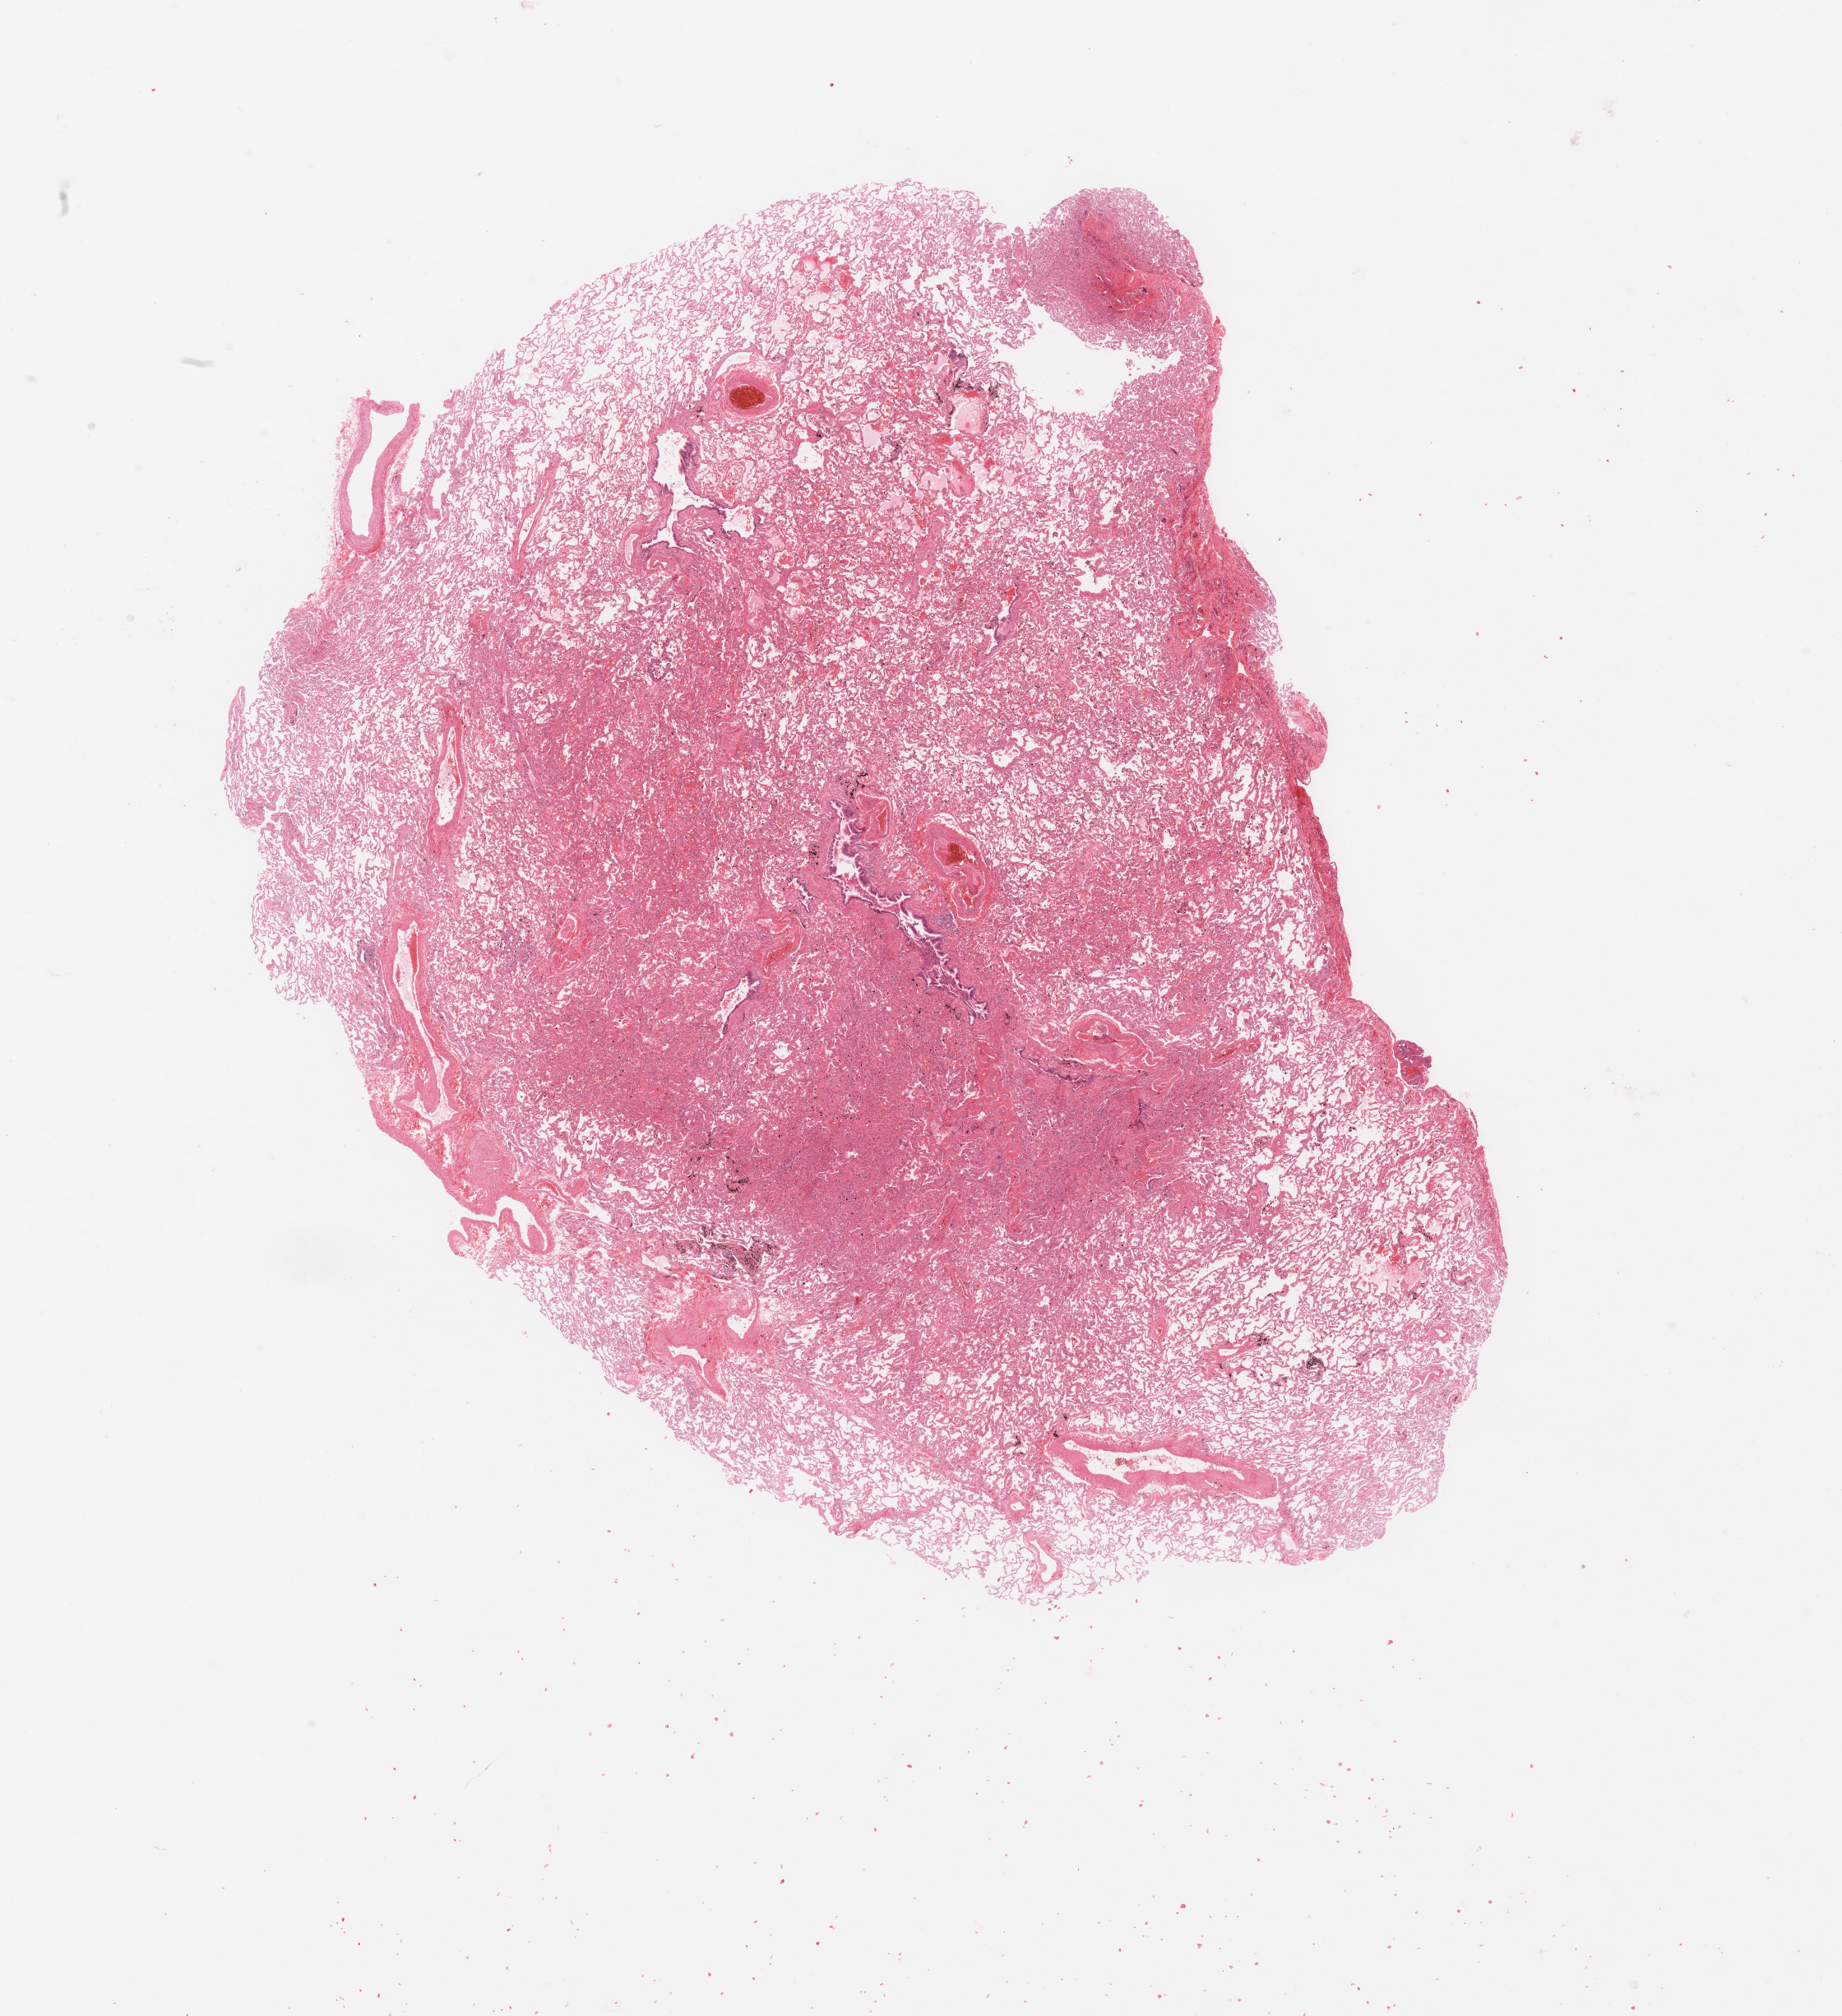
Whole-slide histology image, H&E — whole scanned area (about 17.7 x 19.4 mm, from a 20x scan) shown as a low-resolution overview. Normal (non-tumour) tissue sample, sampled site: lung. 62-year-old female patient.
This section: normal (non-tumour) tissue from the same patient. Patient diagnosis: Adenocarcinoma, NOS.